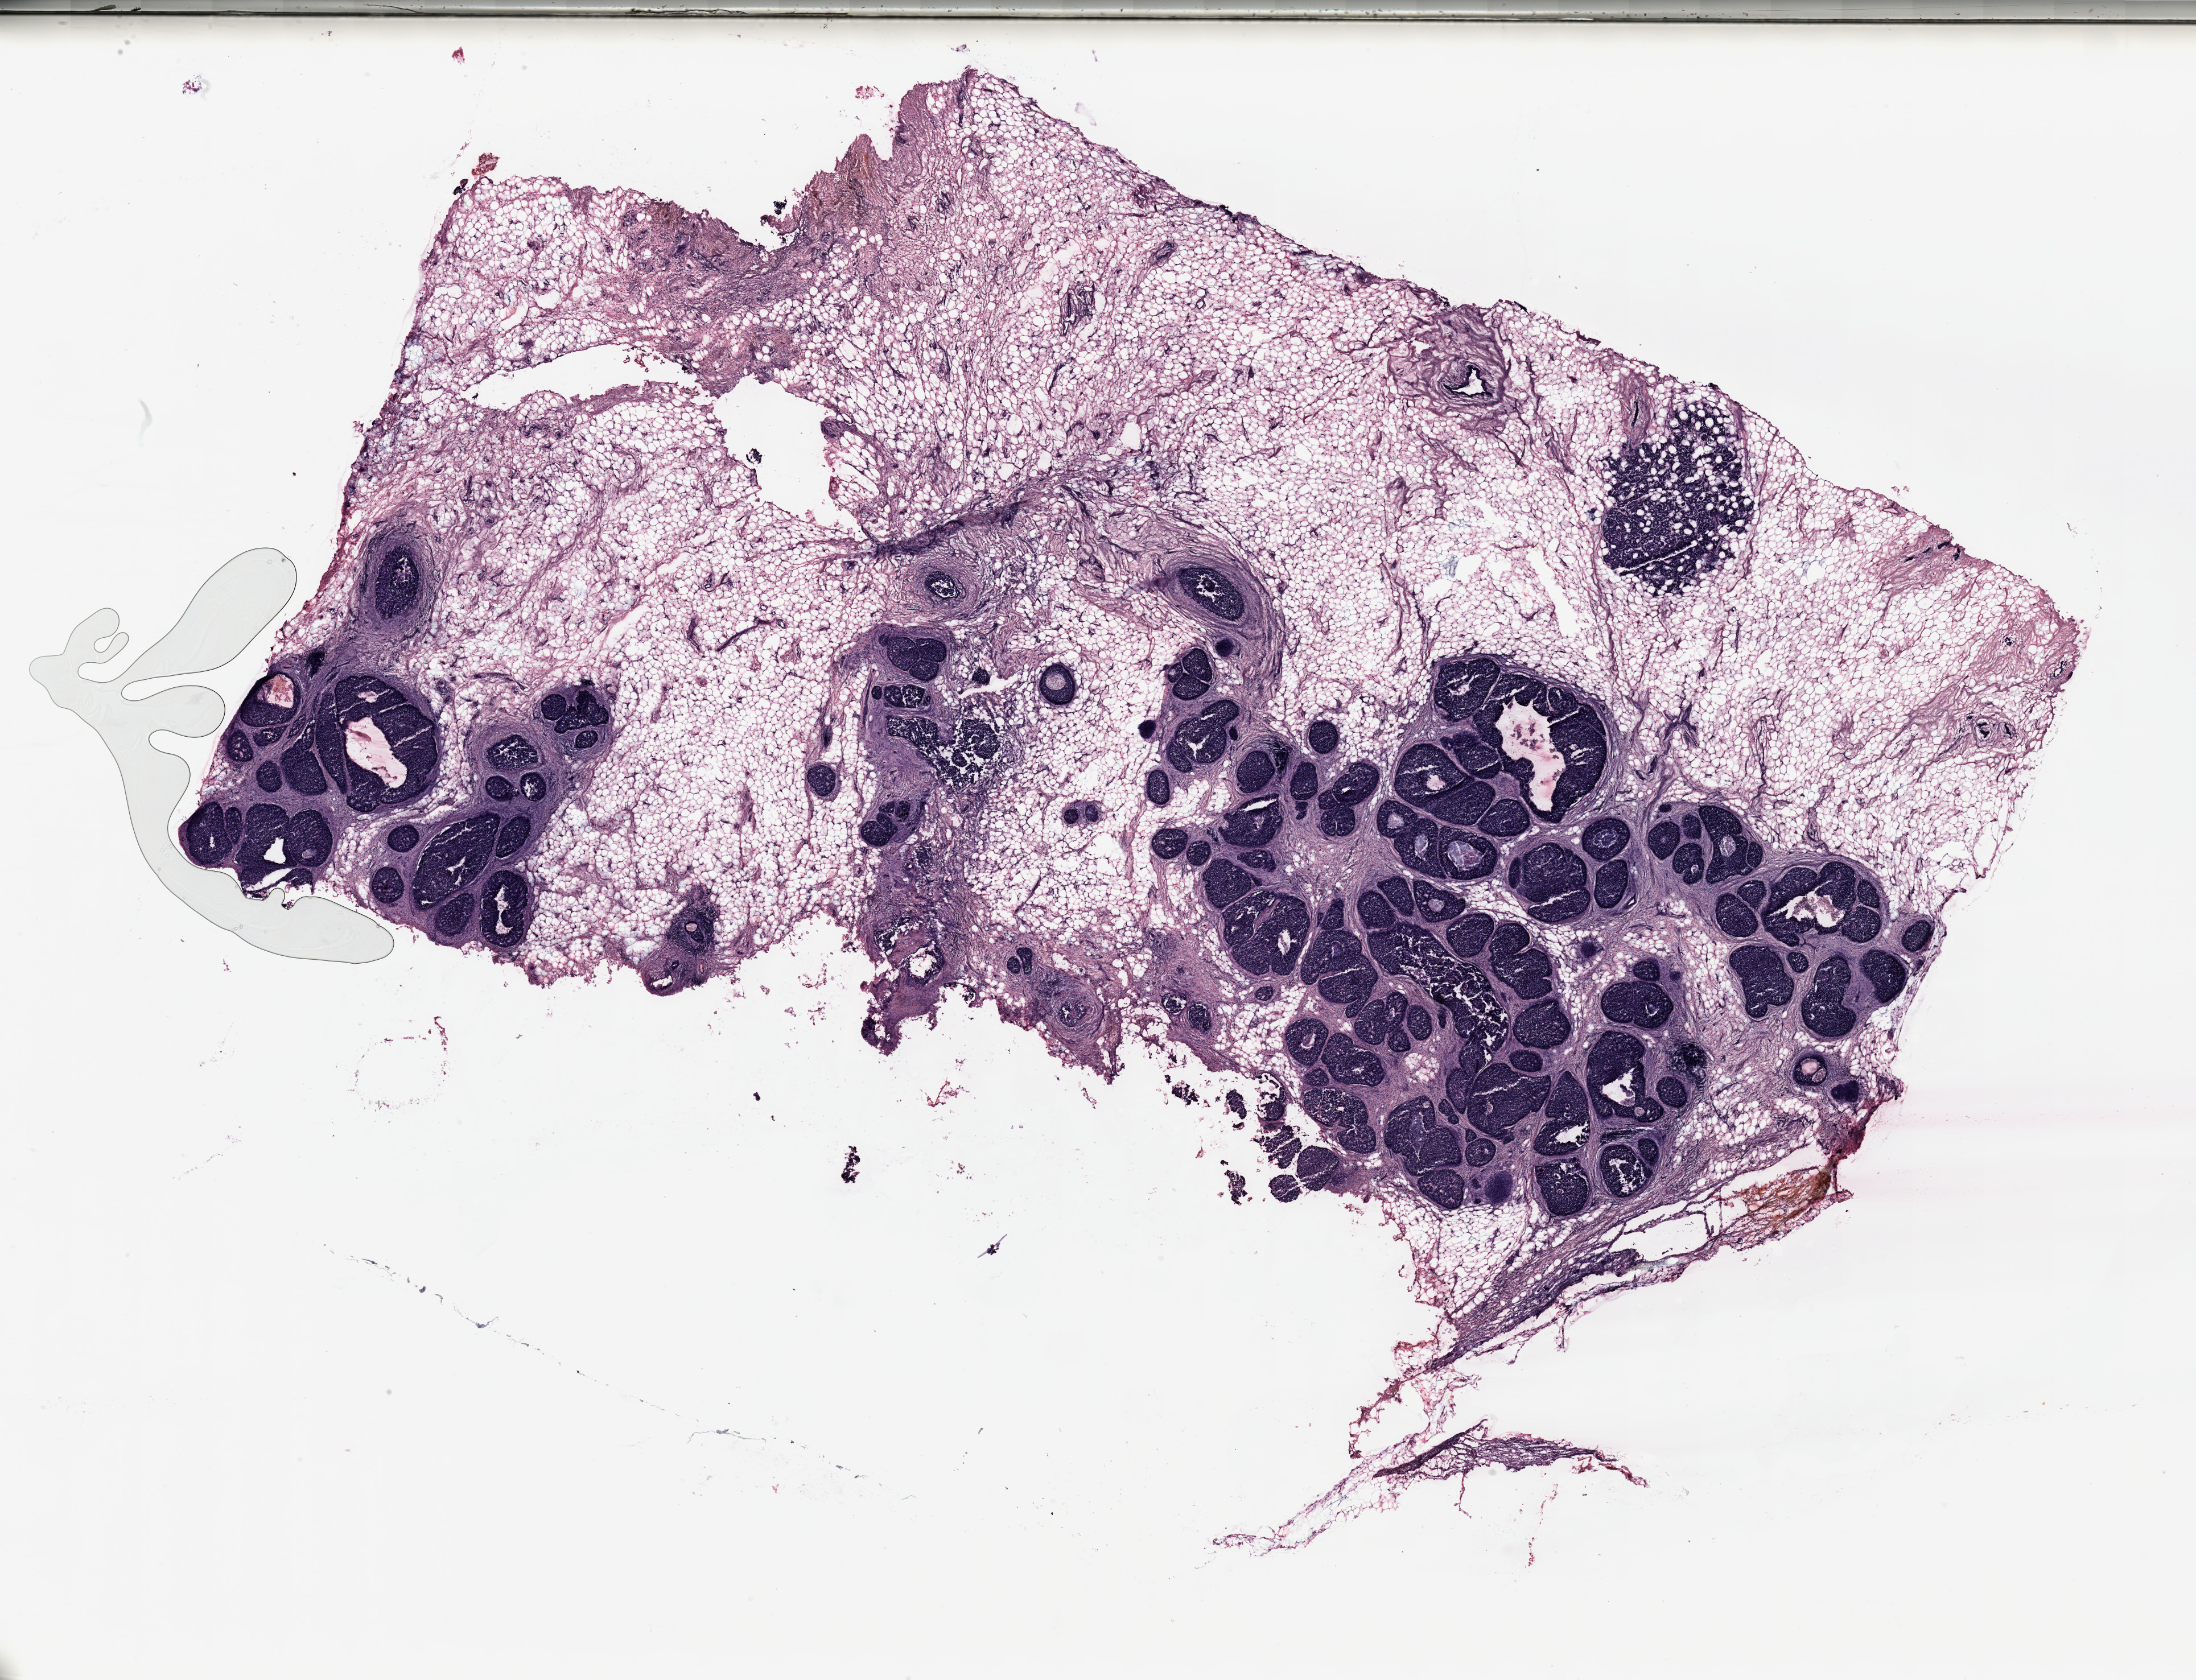
Digitized H&E-stained tissue section (whole slide) — a low-resolution overview of the entire scanned area, about 30.5 x 23.4 mm, tumour tissue sample, breast. Female, 54 y/o.
AJCC pathologic stage: IIA. Histologic diagnosis: Infiltrating duct carcinoma, NOS.